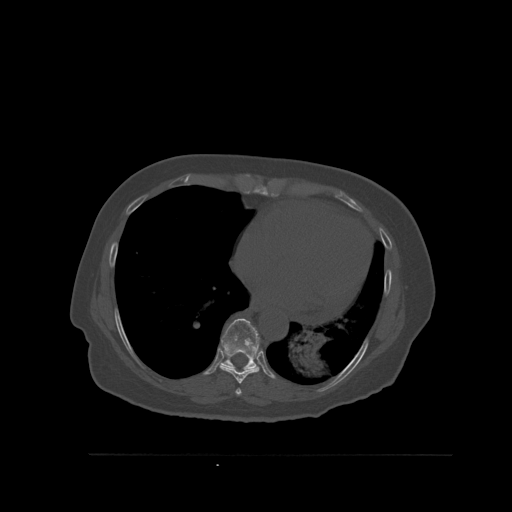
CT including the spine, one axial slice; bone window (W 1800 / L 400 HU); 1.5 mm slice thickness; 512 × 512 image matrix, field of view 470 × 470 mm. Female patient, age 73 years. Case-level facts recorded for this patient, not image findings: primary cancer: breast.
Outlined on this slice (semi-automatic segmentation, software-assisted and operator-edited):
- T7 vertebra: bounding box [x1, y1, x2, y2] px = [235, 388, 242, 396]
- T8 vertebra: [220, 365, 260, 384]
- T9 vertebra: [221, 318, 260, 371]